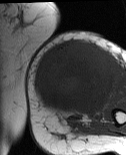
MRI of an extremity soft-tissue mass, one axial slice. Position 27 of 86 along the scan axis. MR volume resampled by the dataset authors to the PET/CT grid (not the native acquisition matrix). 3.27 mm slice thickness. 126 × 155 image matrix, field of view 123 × 151 mm. Female patient. From the clinical record (not read from this slice): histological type: pleiomorphic leiomyosarcoma; grade: high; site of the primary tumour: left biceps.
Annotated regions visible in this slice (expert contour drawn on MRI and transferred to this co-registered scan by the dataset authors):
- gross tumour volume including surrounding oedema: bounding box <34,40,115,116> (left, top, right, bottom; pixels)
- gross tumour volume (mass): <34,40,115,116>